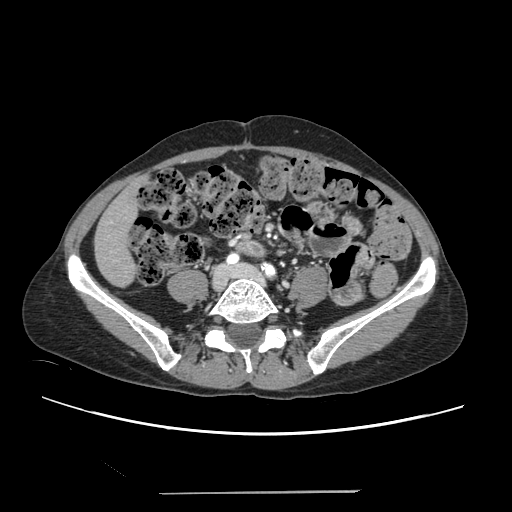
Contrast-enhanced abdominal CT, one axial slice; slice 27 of 240 in the series (ordered by position); intravenous contrast given; soft-tissue window (W 400 / L 40 HU); 1.25 mm slice thickness; 512 × 512 image matrix. Female patient, age 60 years. From the clinical record (not read from this slice): diagnosis: colorectal cancer liver metastases, imaged before liver resection; multiple liver metastases: no; largest metastasis: 1.5 cm; disease in both lobes: no.
Structures marked on this image (expert manual segmentation):
- liver: bounding box <96,182,139,285> (left, top, right, bottom; pixels)
- planned liver remnant (the part of the liver to remain after resection): <96,181,140,285>
- portal vein (with intrahepatic branches): <110,221,112,252>